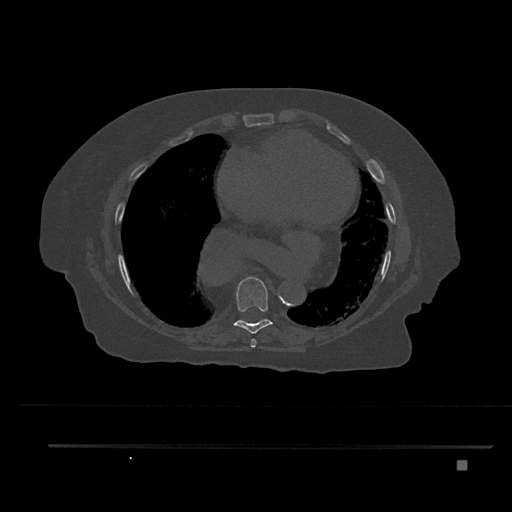
CT including the spine, one axial slice; position 439 of 797 along the scan axis; bone window (W 1800 / L 400 HU); 0.5 mm slice thickness; 512 × 512 image matrix, field of view 437 × 437 mm. Female patient, age 76 years. Case-level facts recorded for this patient, not image findings: primary cancer: lung.
Outlined on this slice (semi-automatically segmented with operator editing):
- T7 vertebra: bounding box (x1, y1, x2, y2) in pixels: (250, 339, 256, 348)
- T8 vertebra: (233, 277, 273, 334)